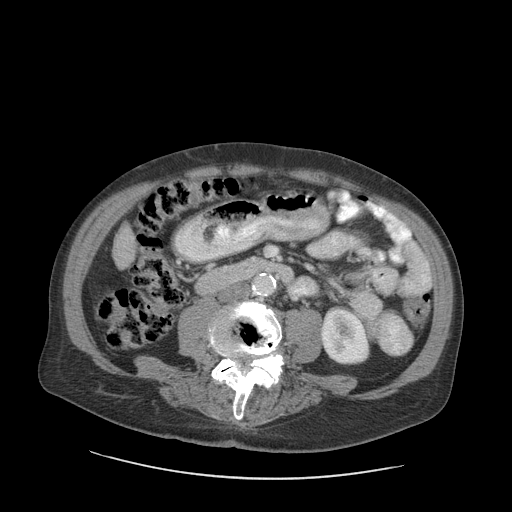
Contrast-enhanced abdominal CT (liver protocol), one axial slice; position 18 of 89 along the scan axis; reconstruction kernel STANDARD; soft-tissue window (W 400 / L 40 HU); 2.5 mm slice thickness; 512 × 512 image matrix. Case-level facts recorded for this patient, not image findings: diagnosis: hepatocellular carcinoma (patient treated with transarterial chemoembolisation; whether this scan precedes or follows treatment is not stated here); TNM stage (as recorded): Stage-I; Child-Pugh class: A; tumour nodularity: uninodular.
Structures marked on this image (semi-automatic segmentation, software-assisted and operator-edited):
- liver parenchyma outside the tumour (the mass and vessels are separate outlines, so this box may not span the whole liver): bounding box [x1, y1, x2, y2] px = [112, 224, 136, 268]